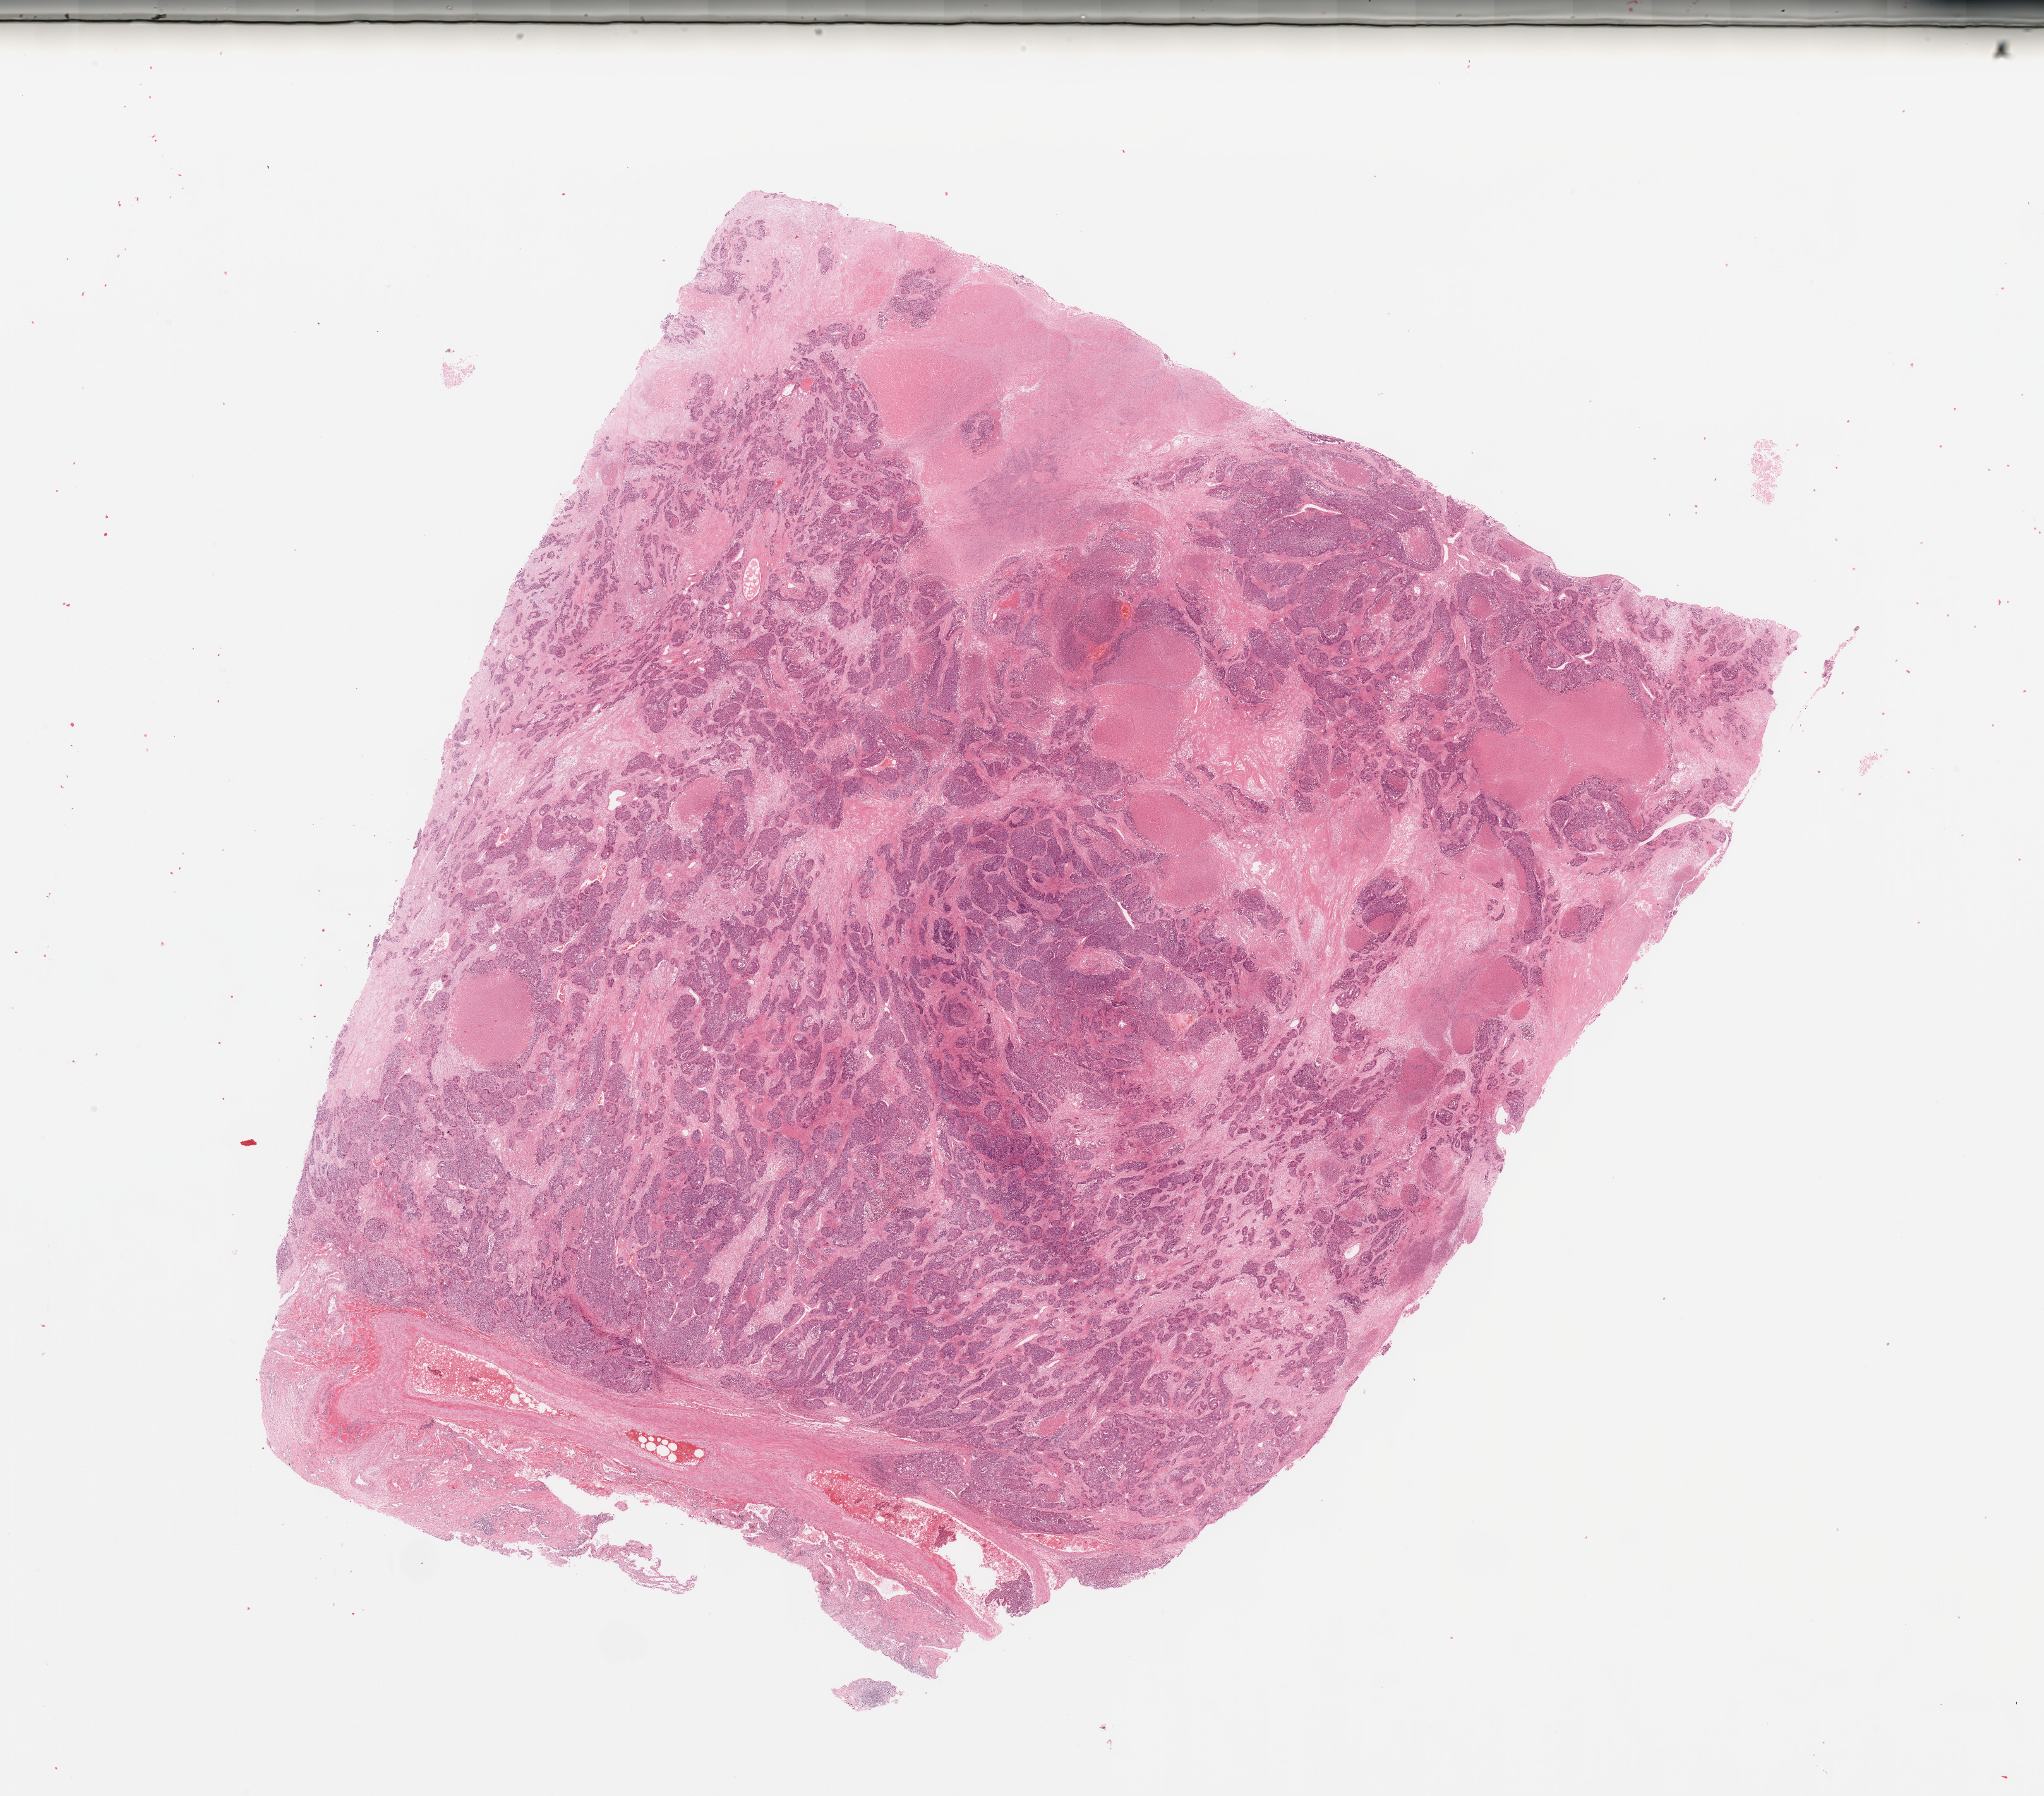
Hematoxylin and eosin (H&E) stained whole-slide image, a low-resolution overview of the entire scanned area, about 25.6 x 22.5 mm (from a 20x scan), lung, tumour tissue. 58-year-old male patient. Histologic grade: G3 (poorly differentiated).
Histologic diagnosis: Adenocarcinoma, NOS. AJCC pathologic stage: IB.